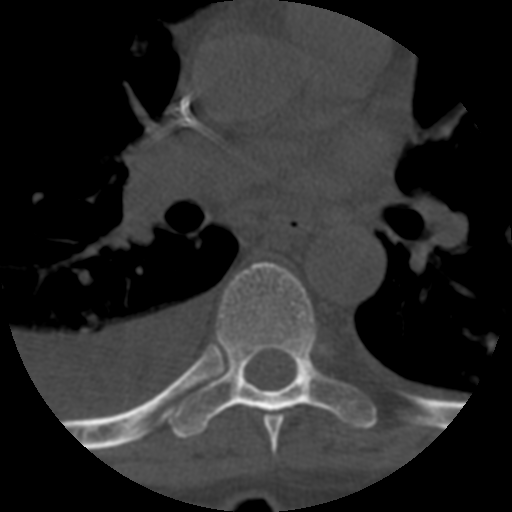
CT including the spine, one axial slice. Position 420 of 708 along the scan axis. Reconstruction kernel STANDARD. One of 3 acquisitions stored at this slice position. Bone window (W 1800 / L 400 HU). 1.25 mm slice thickness. 512 × 512 image matrix. Patient age 55 years. Case-level facts recorded for this patient, not image findings: primary cancer: colon; vertebrae with lytic lesions (as recorded): T12, L1, L5.
Outlined on this slice (semi-automatically segmented with operator editing):
- T6 vertebra: bounding box (x1, y1, x2, y2) in pixels: (263, 415, 284, 455)
- T7 vertebra: (171, 262, 376, 439)